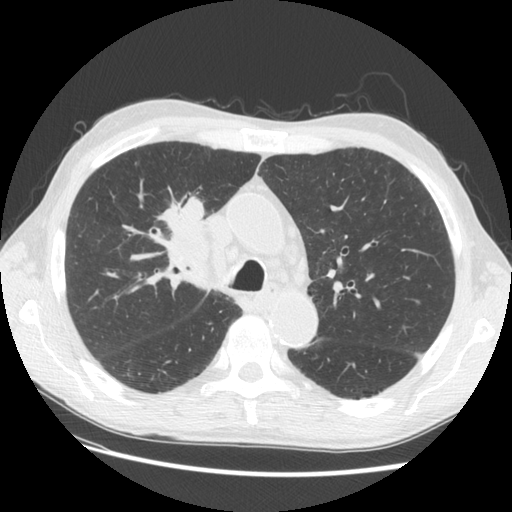
Axial slice from a low-dose chest CT screening exam; third screening round (two years after baseline); lung window (W 1500 / L -600 HU); slice 43 of 133 in the series; 512 × 512 image matrix. Male, age 73 years at enrolment.
Lesion marked by an expert reader, box from (x=141, y=185) to (x=234, y=276) px. The screening reader recorded 4 non-calcified nodules or masses ≥4 mm on this exam (right upper lobe, right upper lobe, right upper lobe, left lower lobe); which of them this box marks is not recorded. Lung cancer was diagnosed 48 days after this screen: squamous cell carcinoma, NOS, right upper lobe, poorly differentiated (G3), stage IIIB (AJCC 6th edition), 56 mm at pathology.